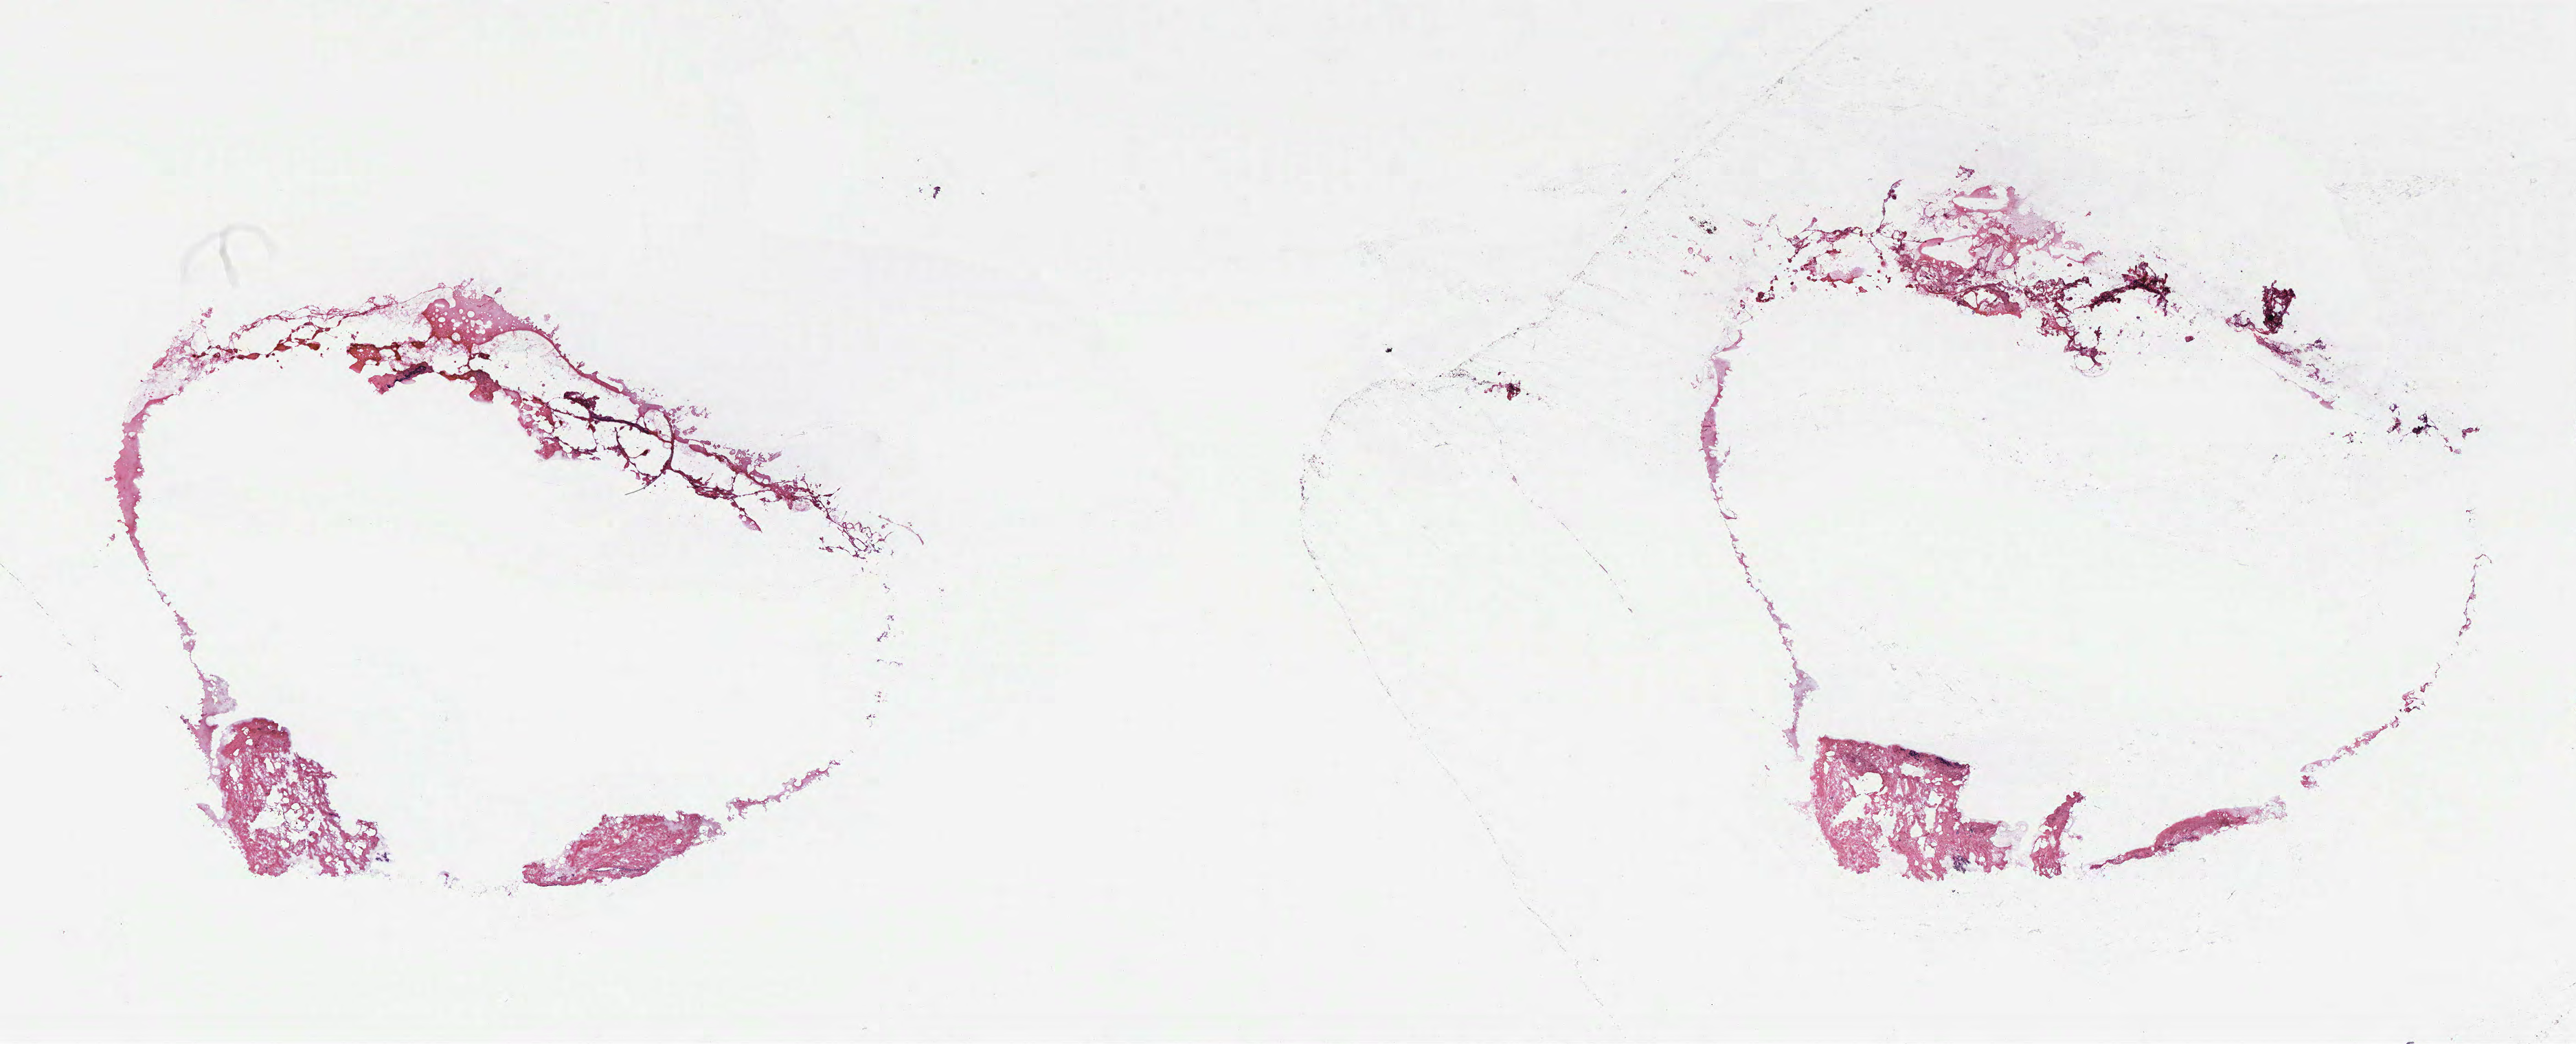
Whole-slide histology image, H&E, a low-resolution overview of the entire scanned area, about 30.0 x 12.2 mm (slide scanned at 40x). Breast, tissue type not recorded.
Patient diagnosis (cohort enrolment): breast cancer (breast).